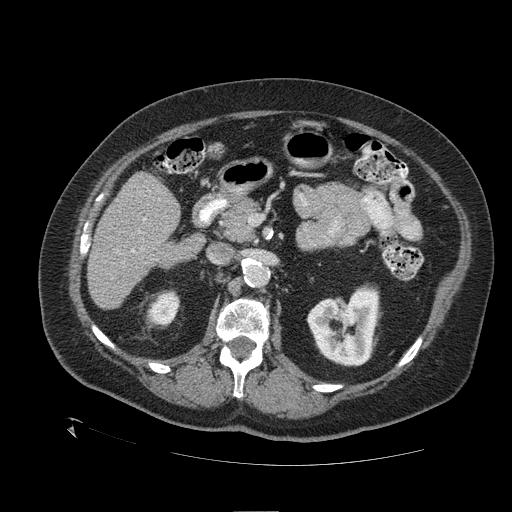
Contrast-enhanced abdominal CT (liver protocol), one axial slice; slice 55 of 109 in the series (ordered by position); reconstruction kernel STANDARD; 120 kVp; one of 2 acquisitions stored at this slice position; soft-tissue window (W 400 / L 40 HU); 2.5 mm slice thickness; 512 × 512 image matrix, field of view 460 × 460 mm. From the clinical record (not read from this slice): diagnosis: hepatocellular carcinoma (patient treated with transarterial chemoembolisation; whether this scan precedes or follows treatment is not stated here); TNM stage (as recorded): Stage-I; Child-Pugh class: A; tumour differentiation: no biopsy; tumour nodularity: uninodular.
Outlined on this slice (semi-automatically segmented with operator editing):
- liver parenchyma outside the tumour (the mass and vessels are separate outlines, so this box may not span the whole liver): bounding box <88,172,201,308> (left, top, right, bottom; pixels)
- liver vessels: <131,218,146,253>